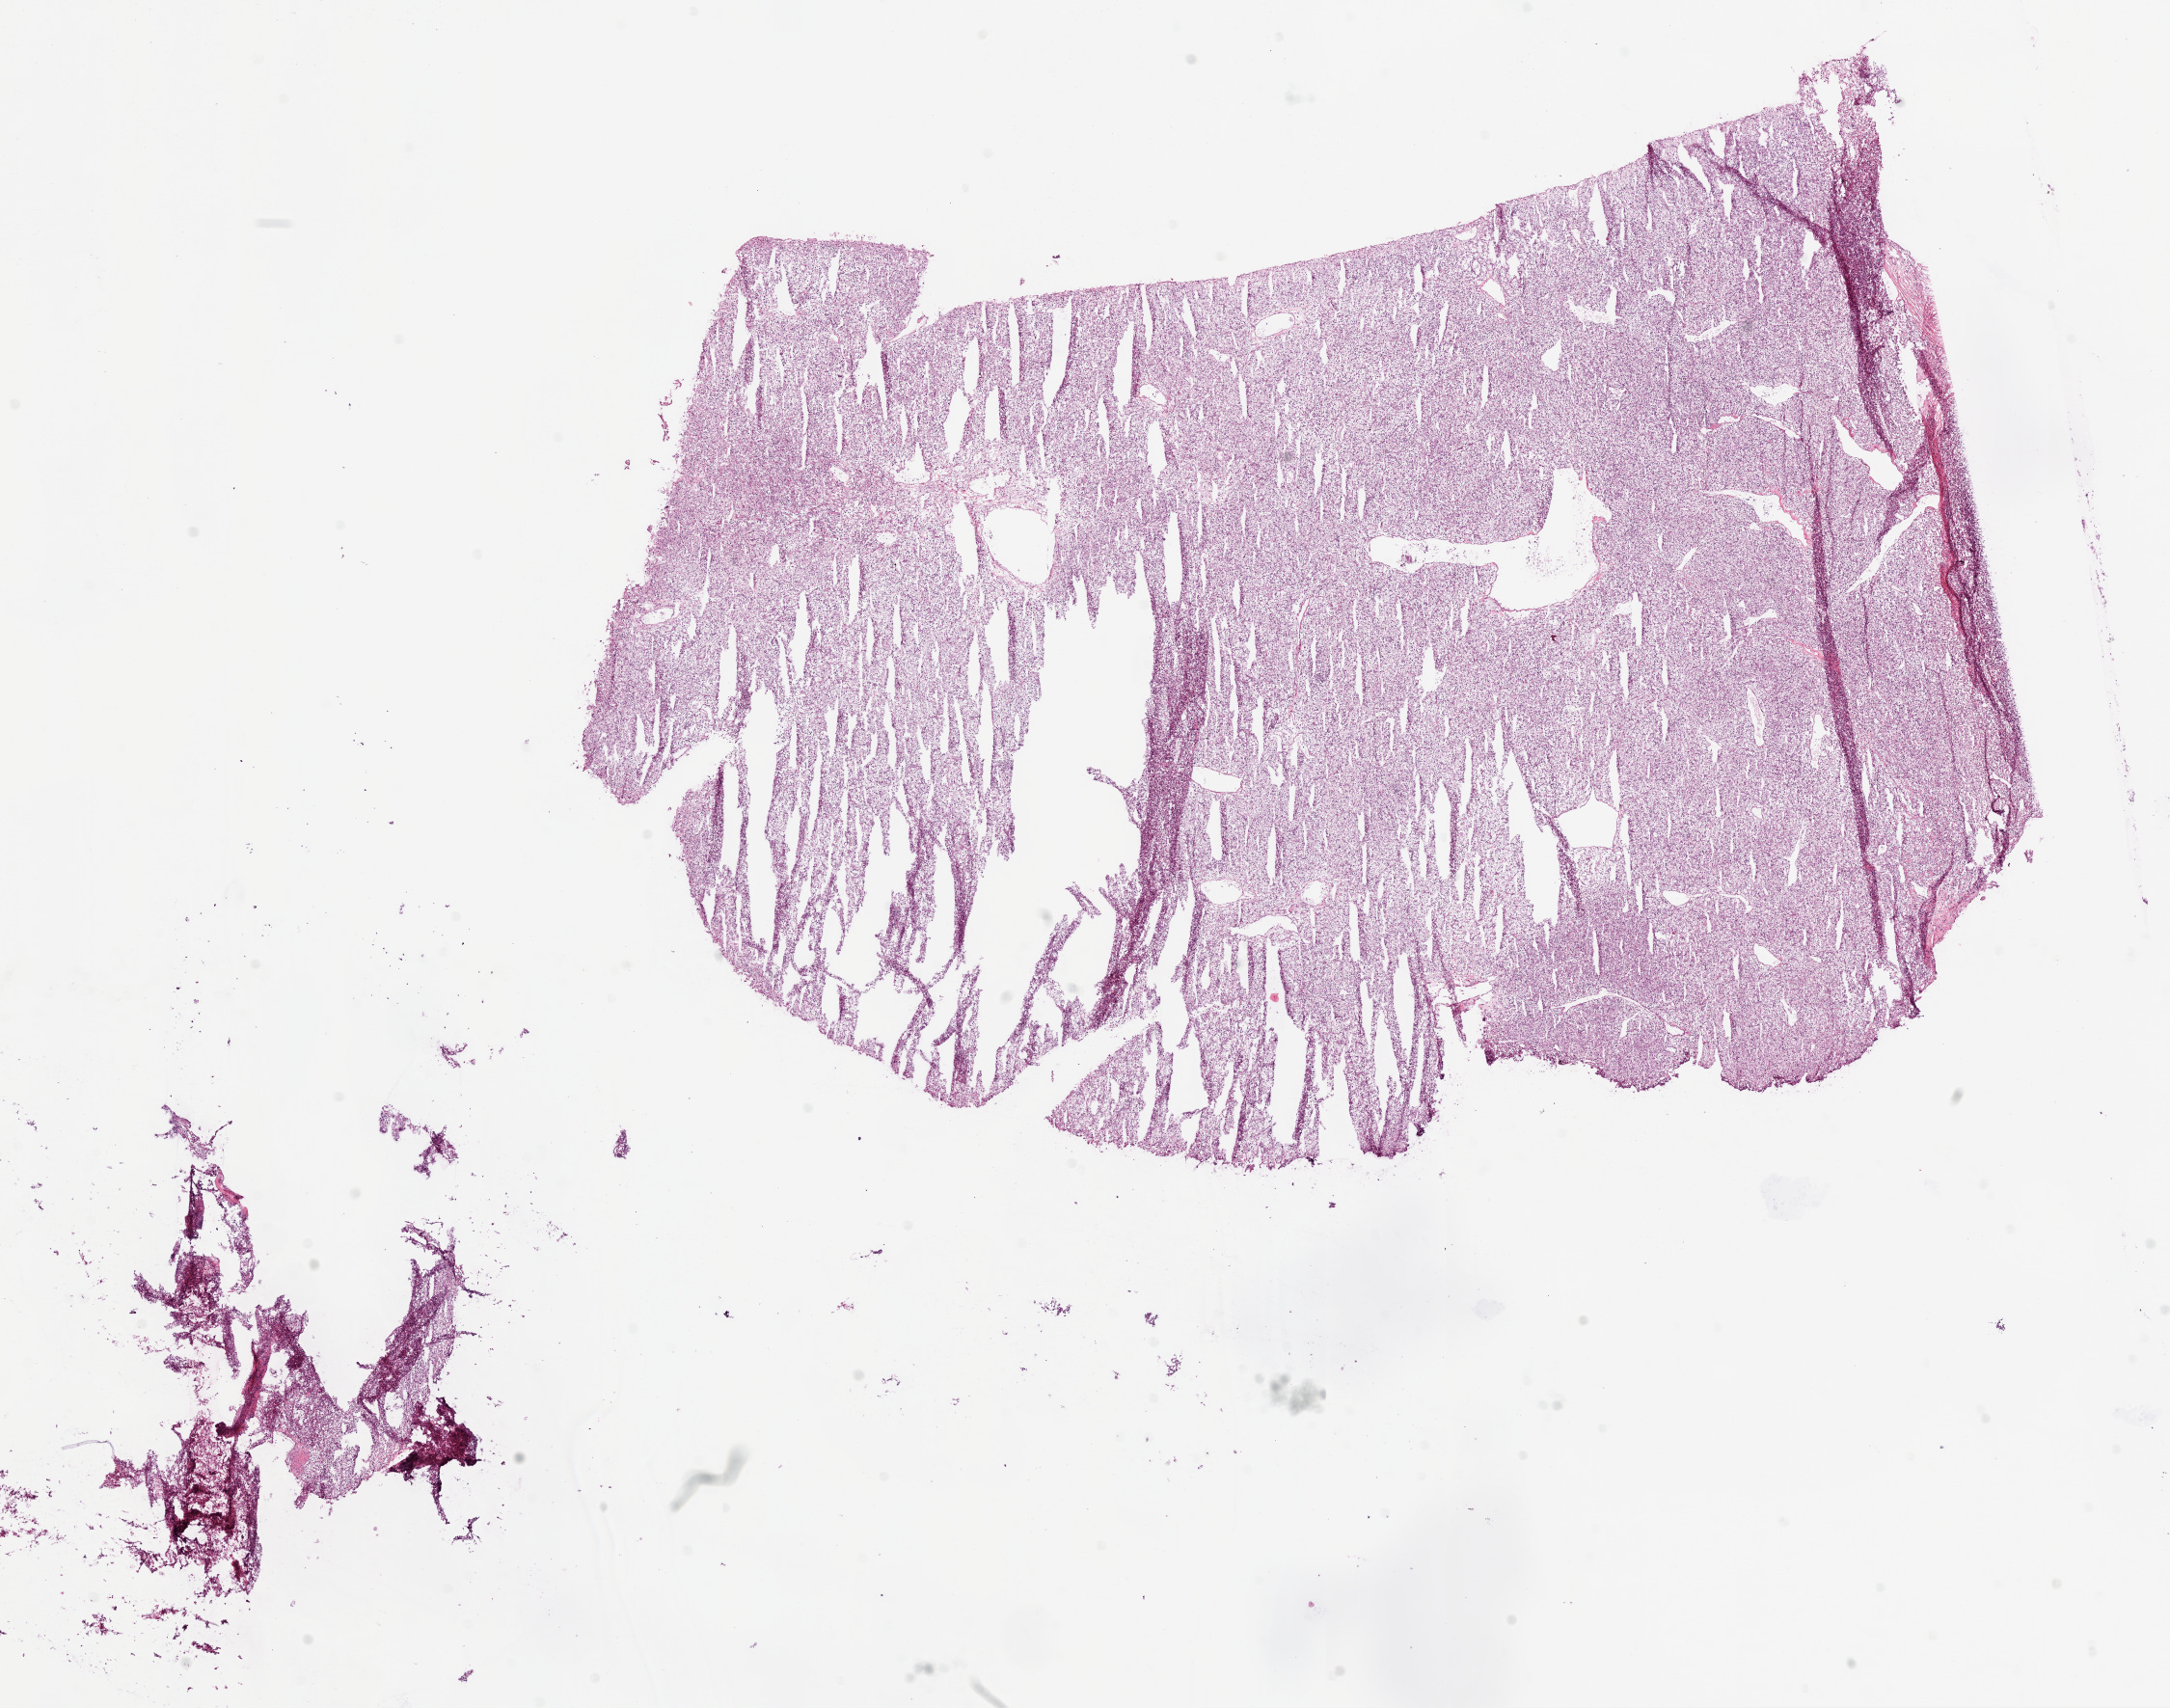
Whole-slide histology image, H&E-stained, whole scanned area (about 18.1 x 14.2 mm) shown as a low-resolution overview. Frozen section from the bottom of the tissue portion. Sample: primary tumour, kidney. Male patient; age at initial diagnosis 74 years. Histologic grade: G3 (poorly differentiated). Composition of this section per pathologist review: tumour cells 95%, tumour nuclei 90%, normal cells 0%, stromal cells 5%, necrosis 0%.
- diagnosis: Clear cell adenocarcinoma, NOS
- laterality: right
- AJCC pathologic stage: I